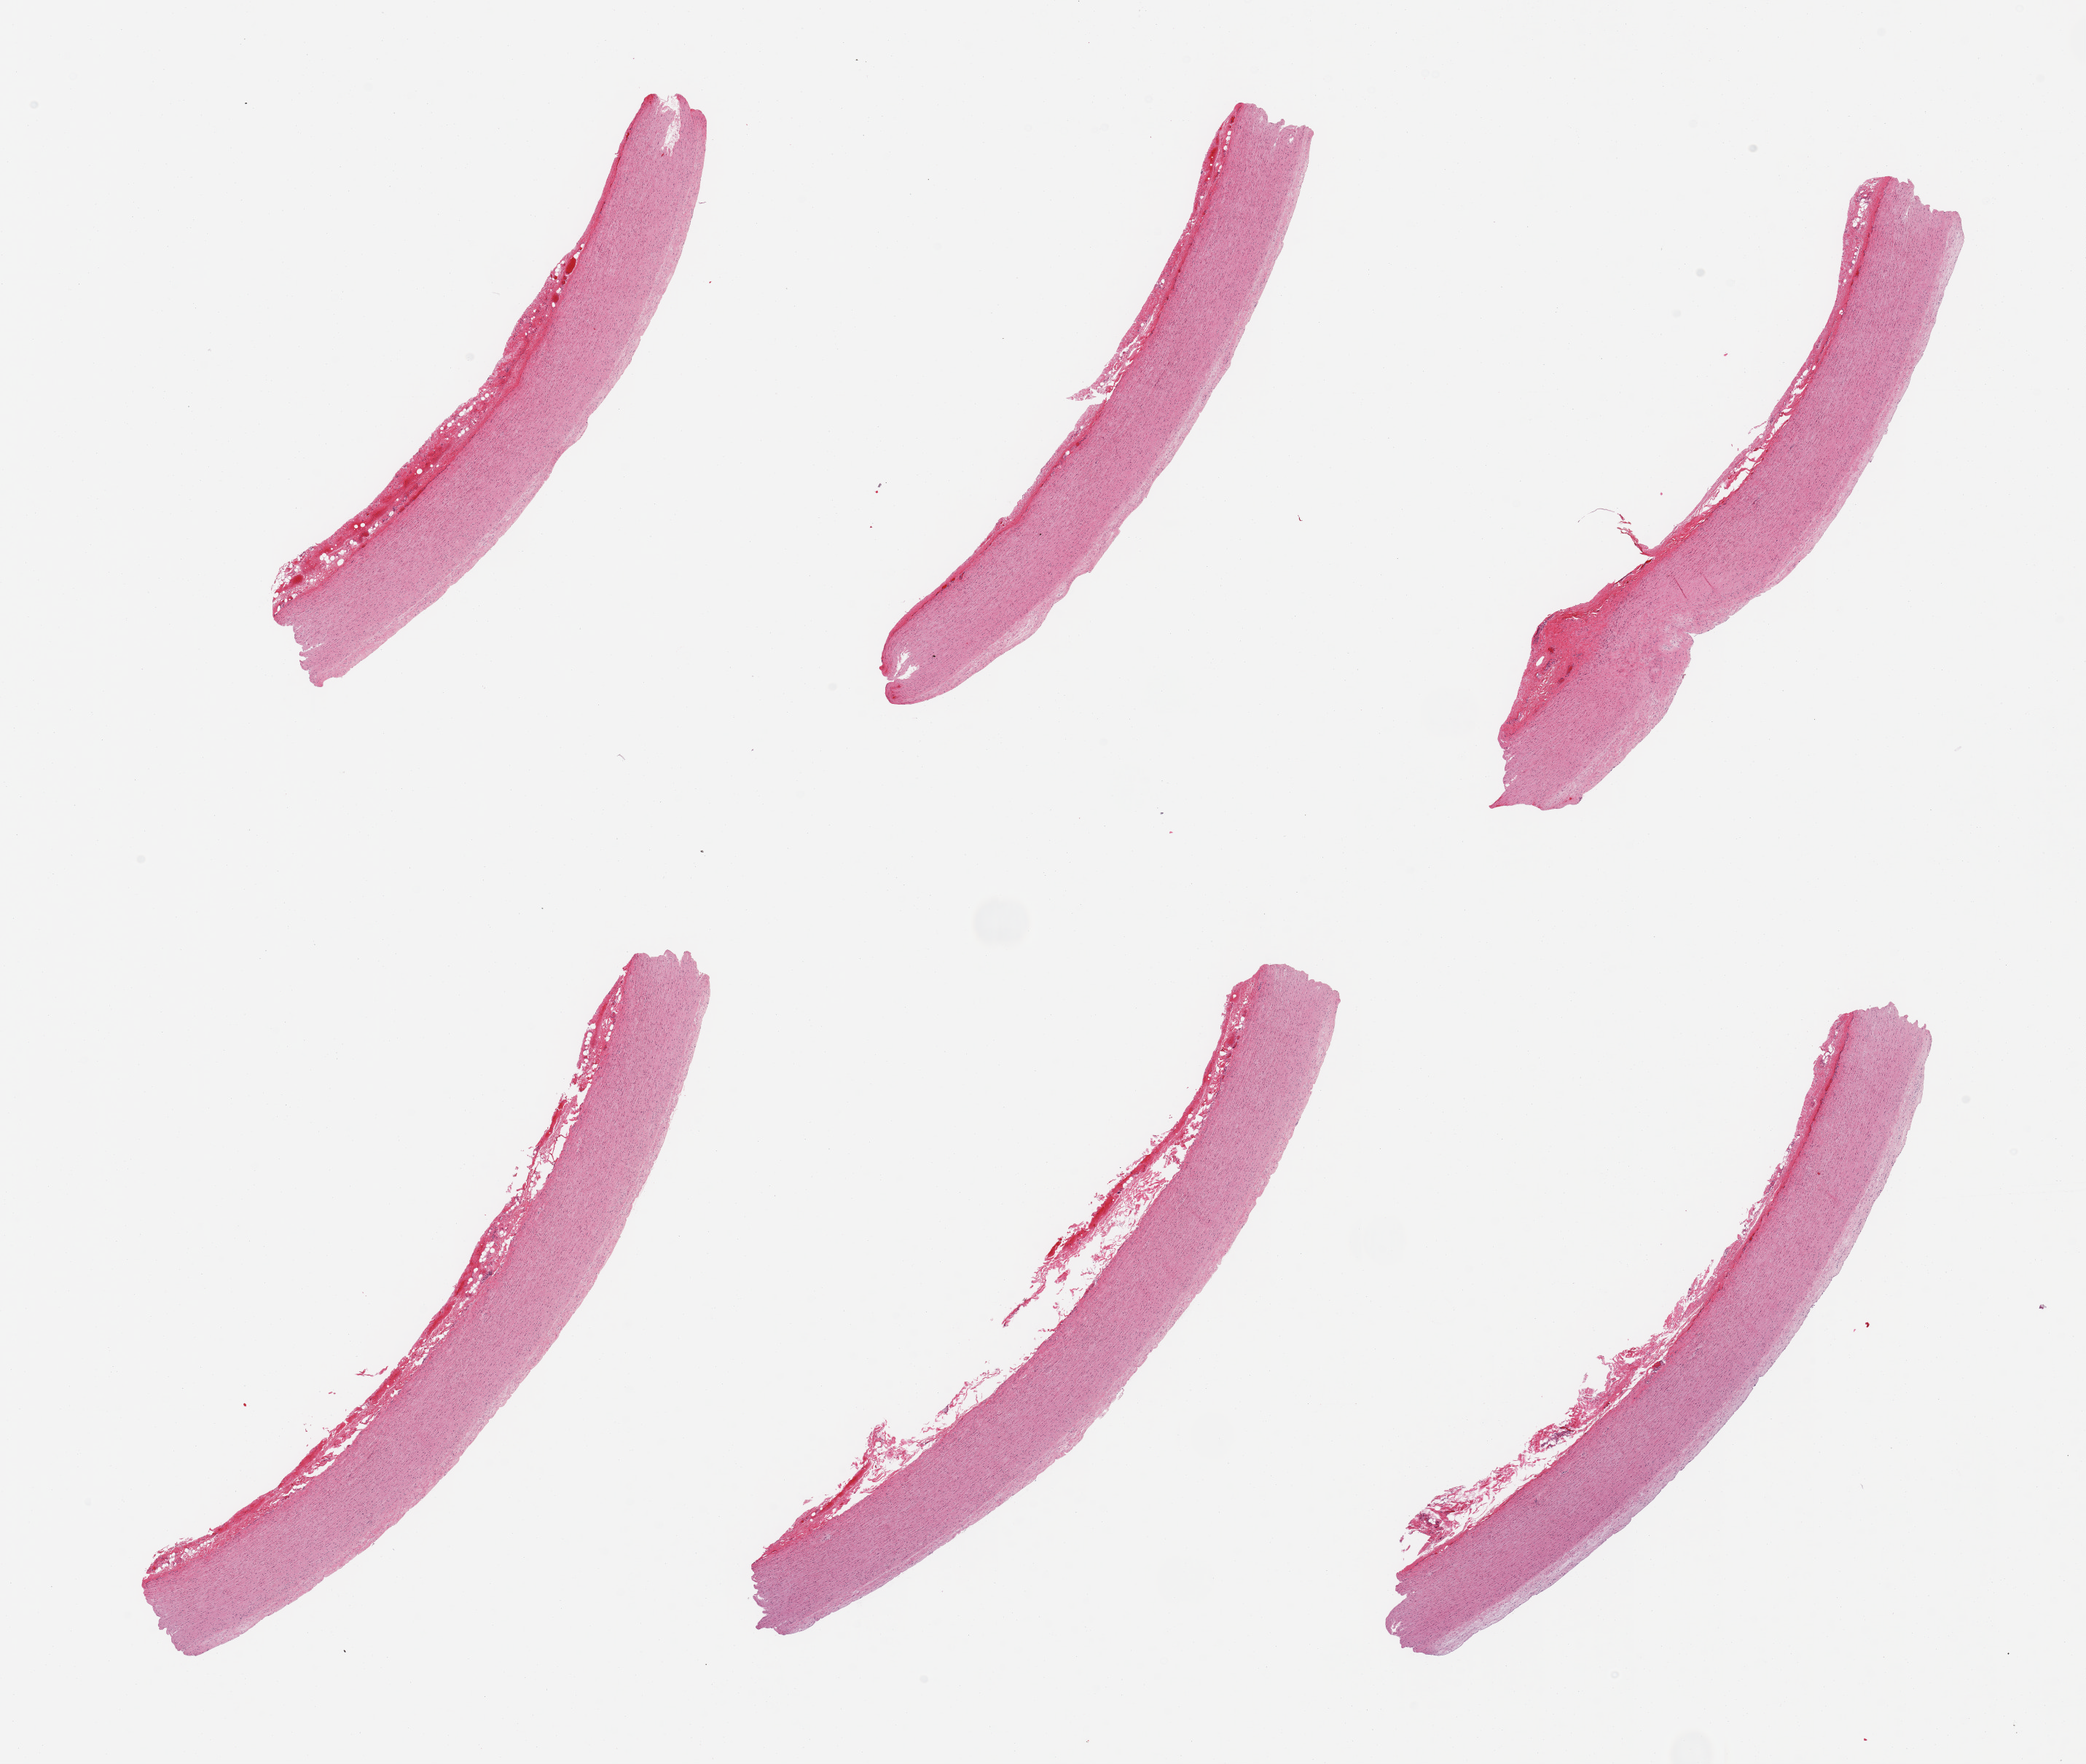
Digitized hematoxylin and eosin (H&E)-stained section, brightfield, whole scanned area (about 22.6 x 19.1 mm) shown as a low-resolution overview; PAXgene-fixed paraffin-embedded (PFPE) section; section of aorta (target tissue); donor tissue sample. Male donor.
Reviewer comment on this tissue sample: 6 pieces; attached adventitia up to 0.65mm; evolving sclerotic plaque.